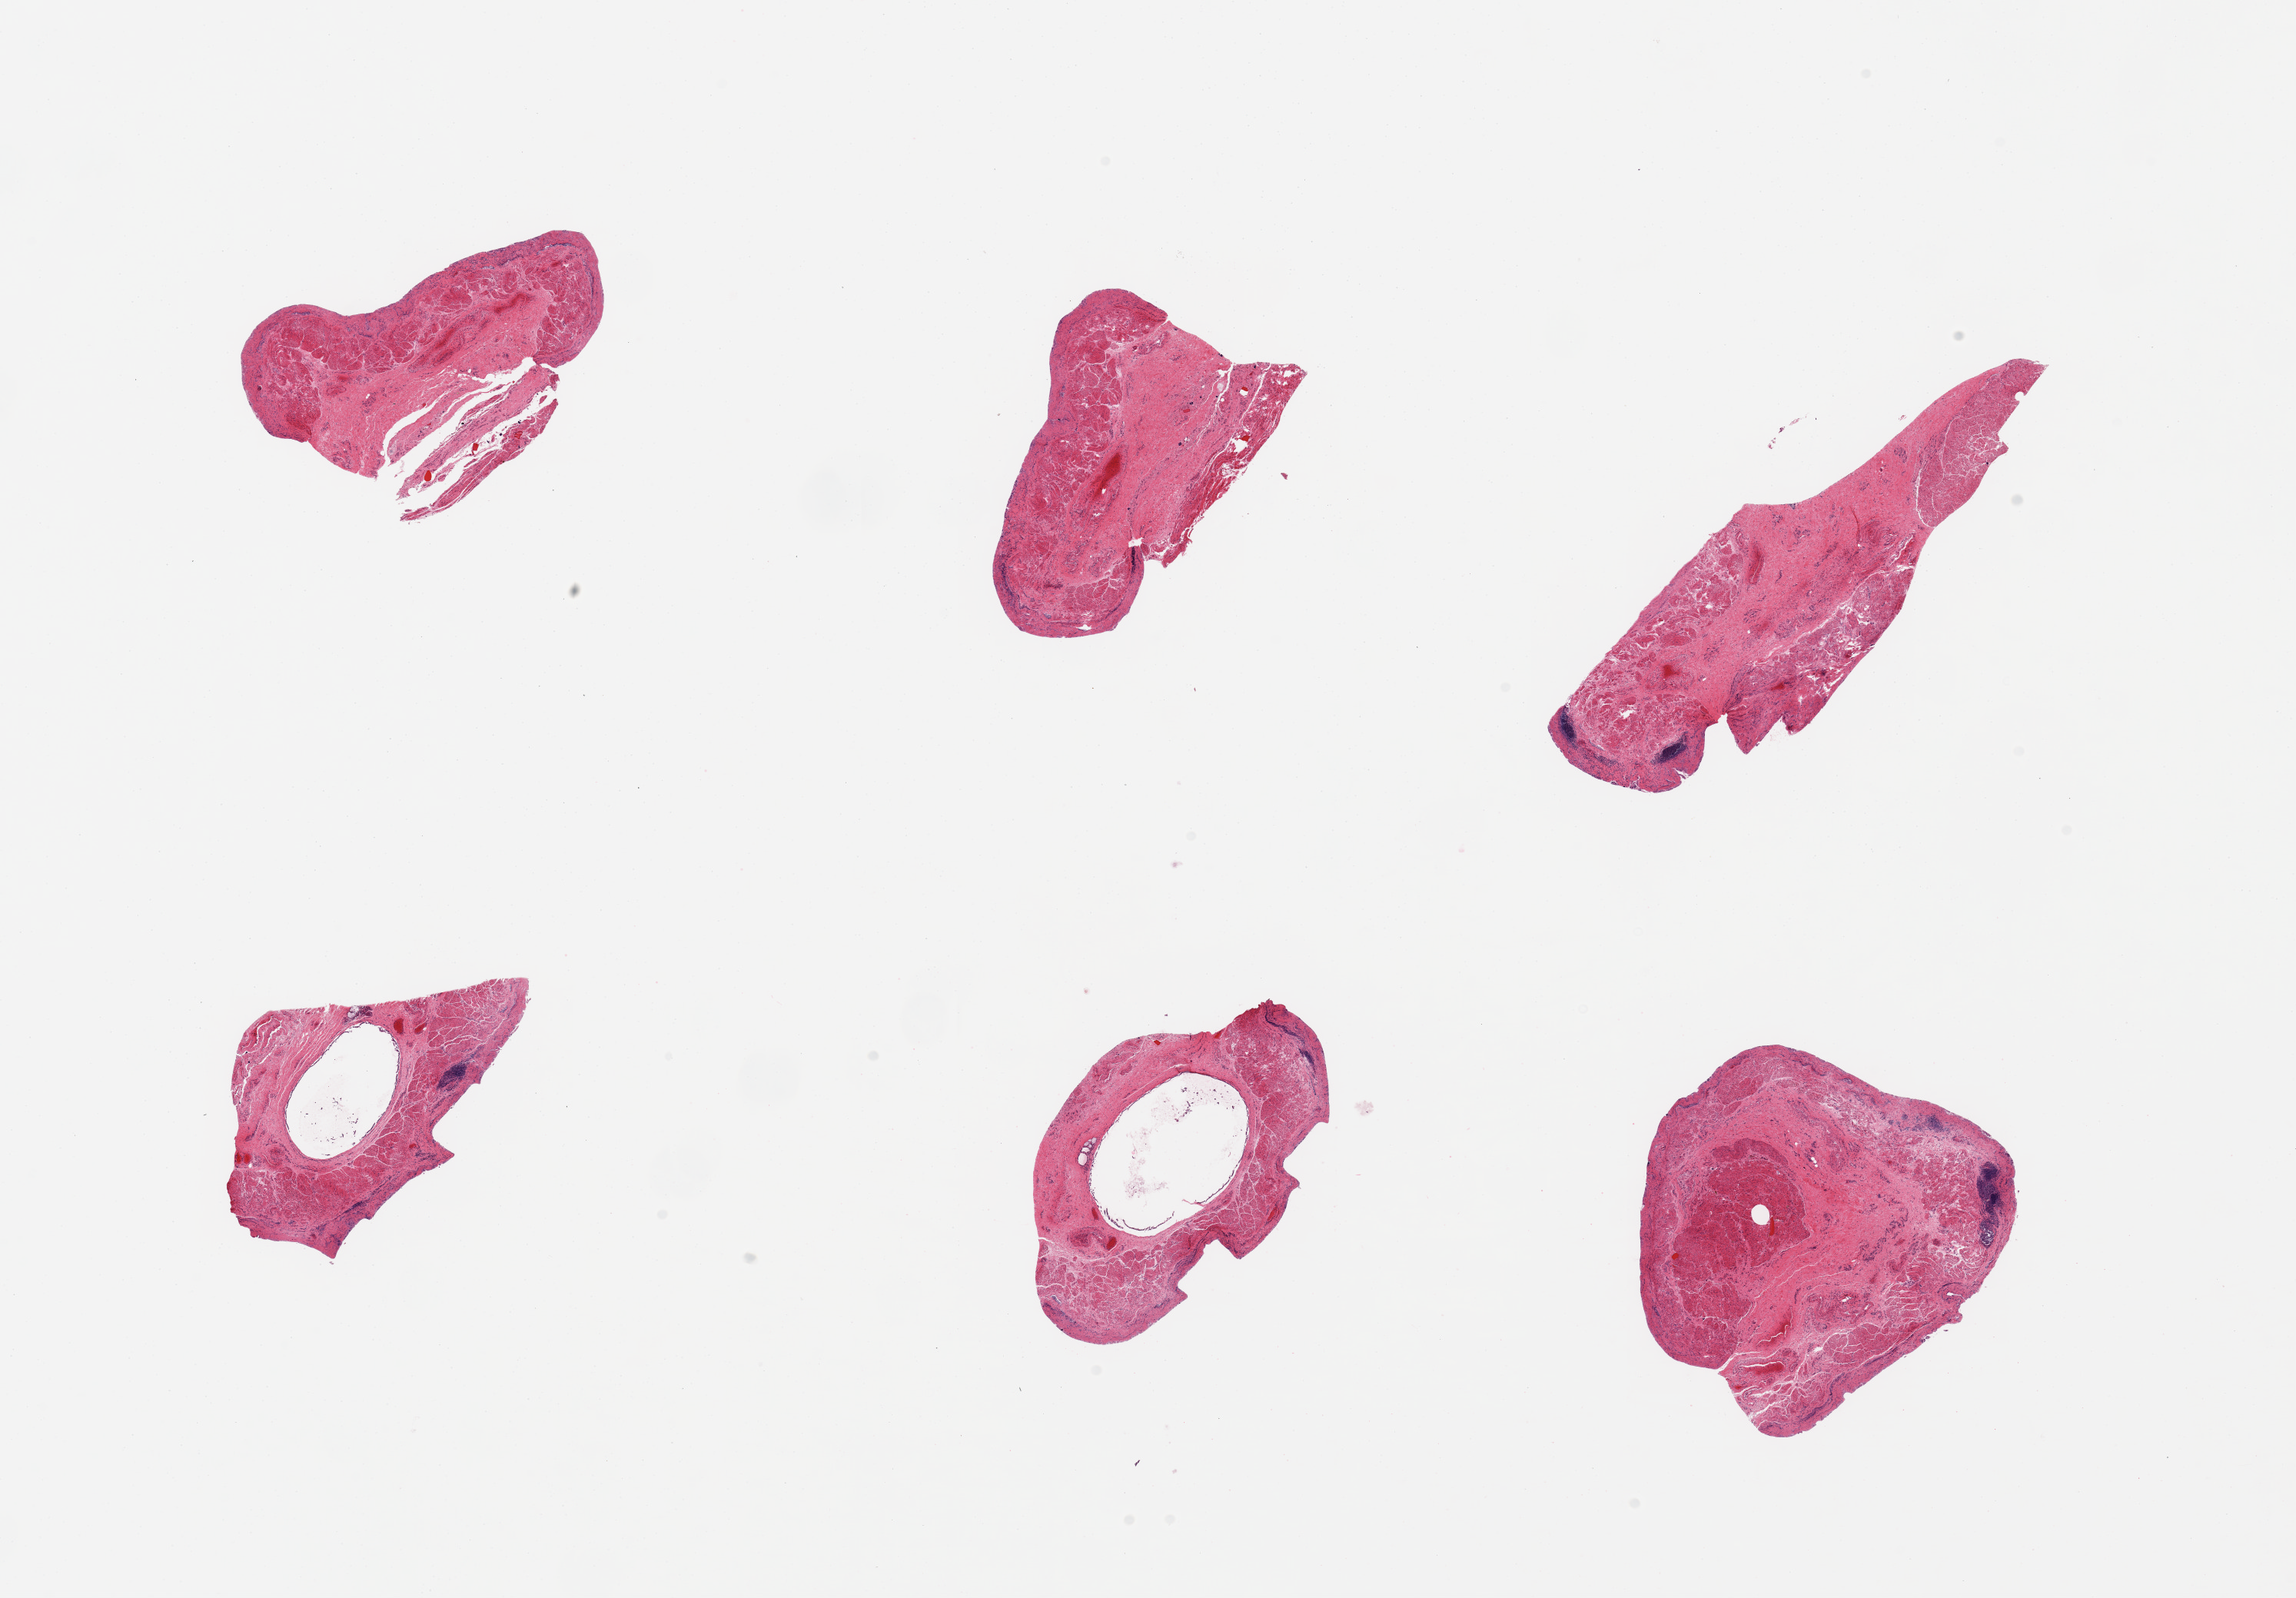
Whole-slide image, hematoxylin and eosin (H&E) stain, brightfield, a low-resolution overview of the entire scanned area, about 23.6 x 16.4 mm (from a 20x scan); PAXgene-fixed, paraffin-embedded tissue; section of esophageal mucous membrane (target tissue); tissue donor sample. Donor: male.
* reviewer comment on this tissue sample: 6 pieces, no squamous epithelium seen, pseudodiverticulosis